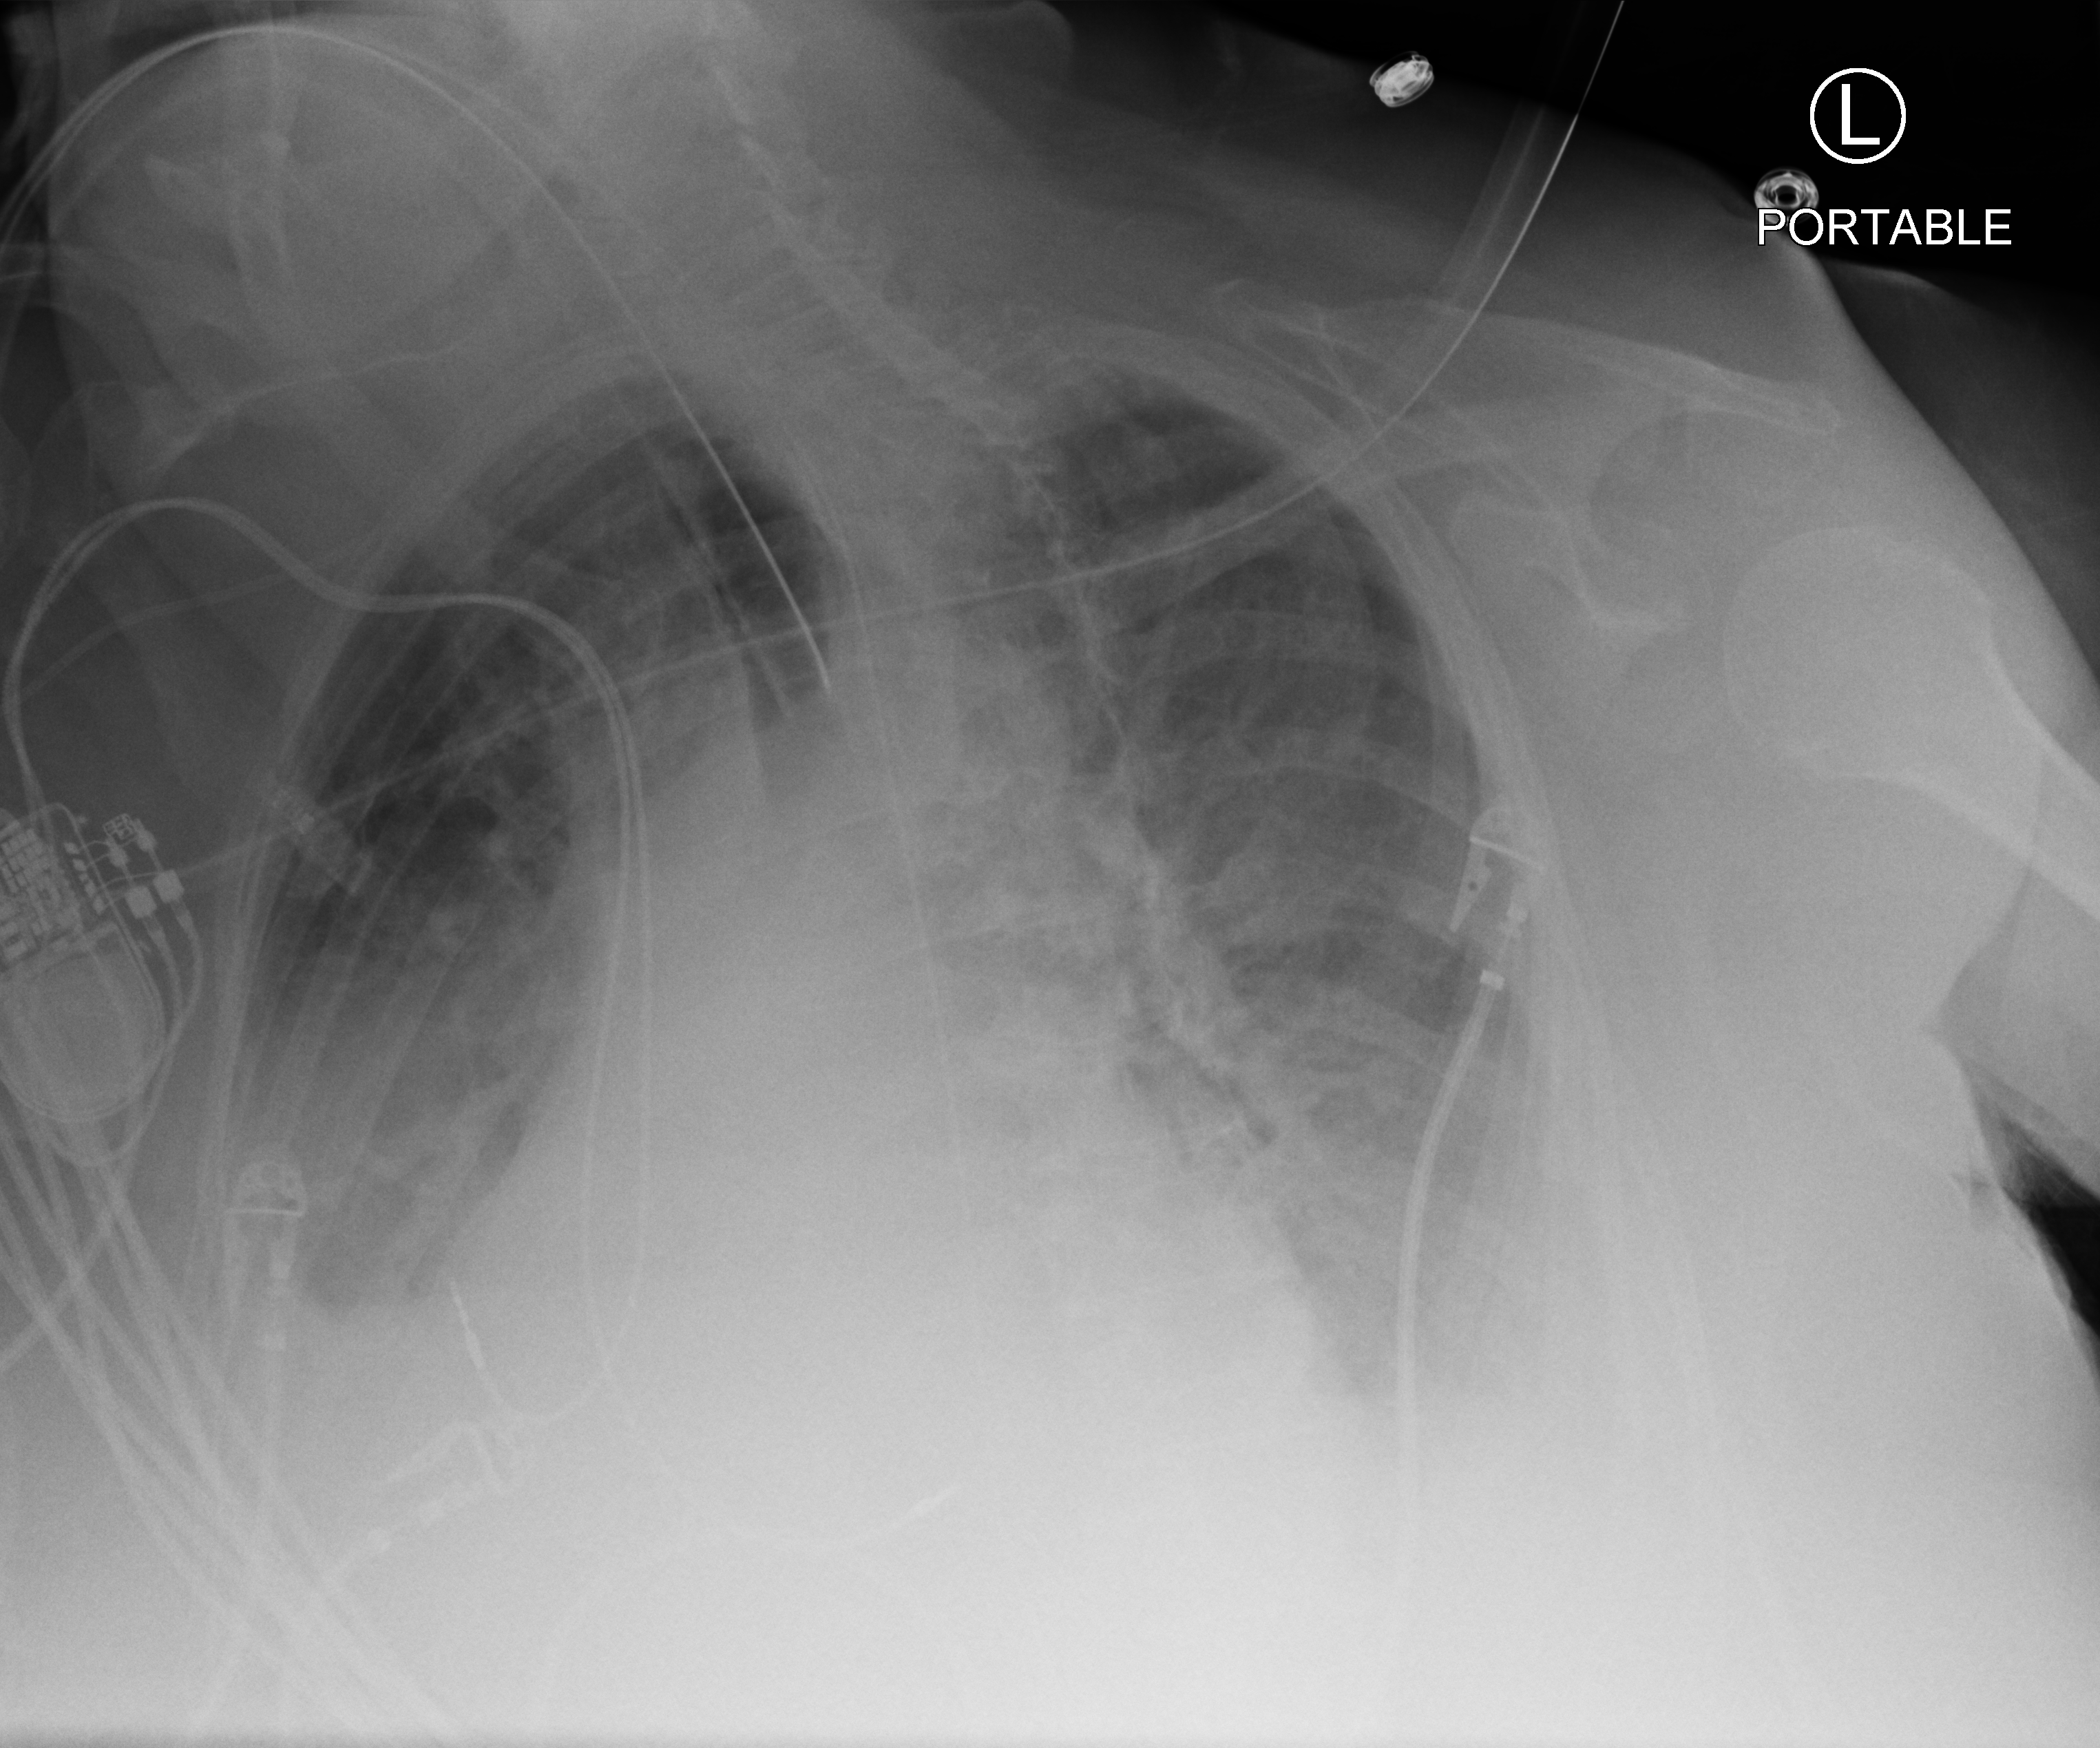
Chest X-ray (portable); anteroposterior (AP) projection. Patient hospitalised with COVID-19; female, aged 75–90 years.
Admission-level facts for this patient (not findings on this image; timing relative to this image not recorded):
- mechanically ventilated during this hospital stay: yes
- other chronic lung disease (admission record): yes